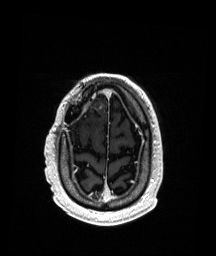
Brain MRI from a brain-tumour surgery series, one axial slice; slice 37 of 192 in the series (ordered by position); T1-weighted post-contrast; 1 mm slice thickness; 216 × 256 image matrix, field of view 211 × 250 mm. From the clinical record (not read from this slice): histopathology: Astrocytoma; WHO grade: 3; IDH mutation: yes; tumour location: Right Frontal.
Annotated regions visible in this slice (manually delineated by an expert):
- previous resection cavity: bounding box <82,106,99,118> (left, top, right, bottom; pixels)